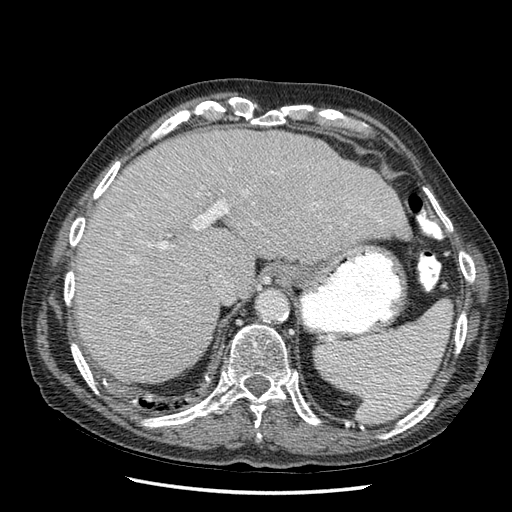
Contrast-enhanced abdominal CT (liver protocol), one axial slice; reconstruction kernel STANDARD; 120 kVp; soft-tissue window (W 400 / L 40 HU); 2.5 mm slice thickness; 512 × 512 image matrix. From the clinical record (not read from this slice): diagnosis: hepatocellular carcinoma (patient treated with transarterial chemoembolisation; whether this scan precedes or follows treatment is not stated here); TNM stage (as recorded): Stage-I; Child-Pugh class: A; tumour nodularity: uninodular.
Structures marked on this image (semi-automatically segmented with operator editing):
- liver parenchyma outside the tumour (the mass and vessels are separate outlines, so this box may not span the whole liver): bounding box [x1, y1, x2, y2] px = [76, 128, 410, 384]
- liver vessels: [118, 169, 363, 318]